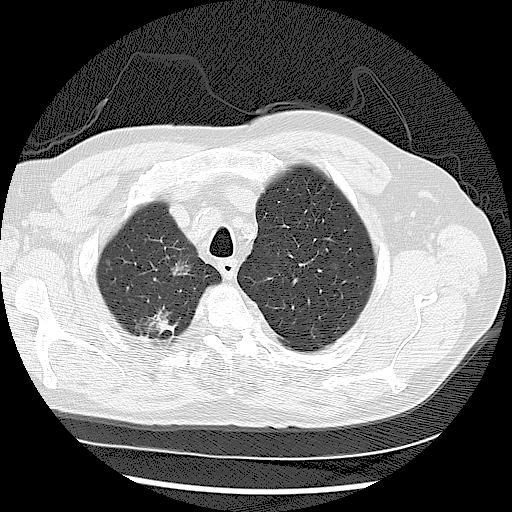
Low-dose screening chest CT, one axial slice; 120 kVp; lung window (W 1500 / L -600 HU); 512 × 512 image matrix.
Structures marked on this image (manually delineated by an expert):
- lesion 1 (tumor, upper lobe of right lung): box from (x=147, y=311) to (x=175, y=333) px